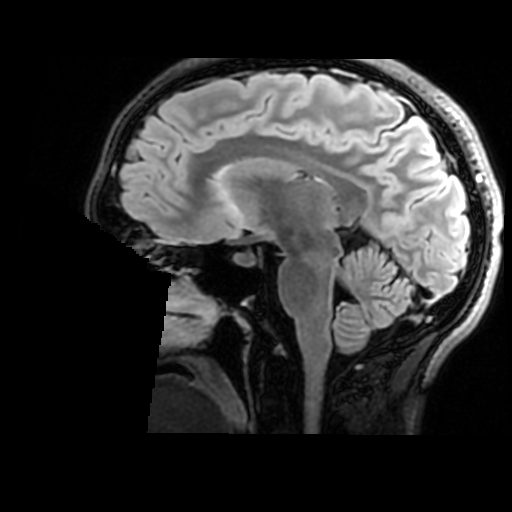
Brain MRI from a brain-tumour surgery series, one sagittal slice; position 94 of 176 along the scan axis; T2 FLAIR; 1 mm slice thickness; 512 × 512 image matrix, field of view 240 × 240 mm. Case-level facts recorded for this patient, not image findings: histopathology: Astrocytoma; WHO grade: 2; IDH mutation: yes.
Outlined on this slice (manually delineated by an expert):
- tumour: box from (x=210, y=182) to (x=239, y=214) px